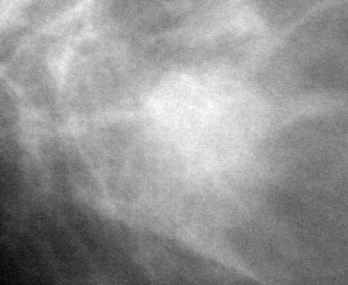
Crop from a digitized film mammogram around one marked abnormality; right breast; MLO view.
Finding: mass, shape round, margins microlobulated; BI-RADS assessment category 3; subtlety rating 5 on a 1 (subtle) to 5 (obvious) scale; benign; no additional work-up was recommended (benign without callback).